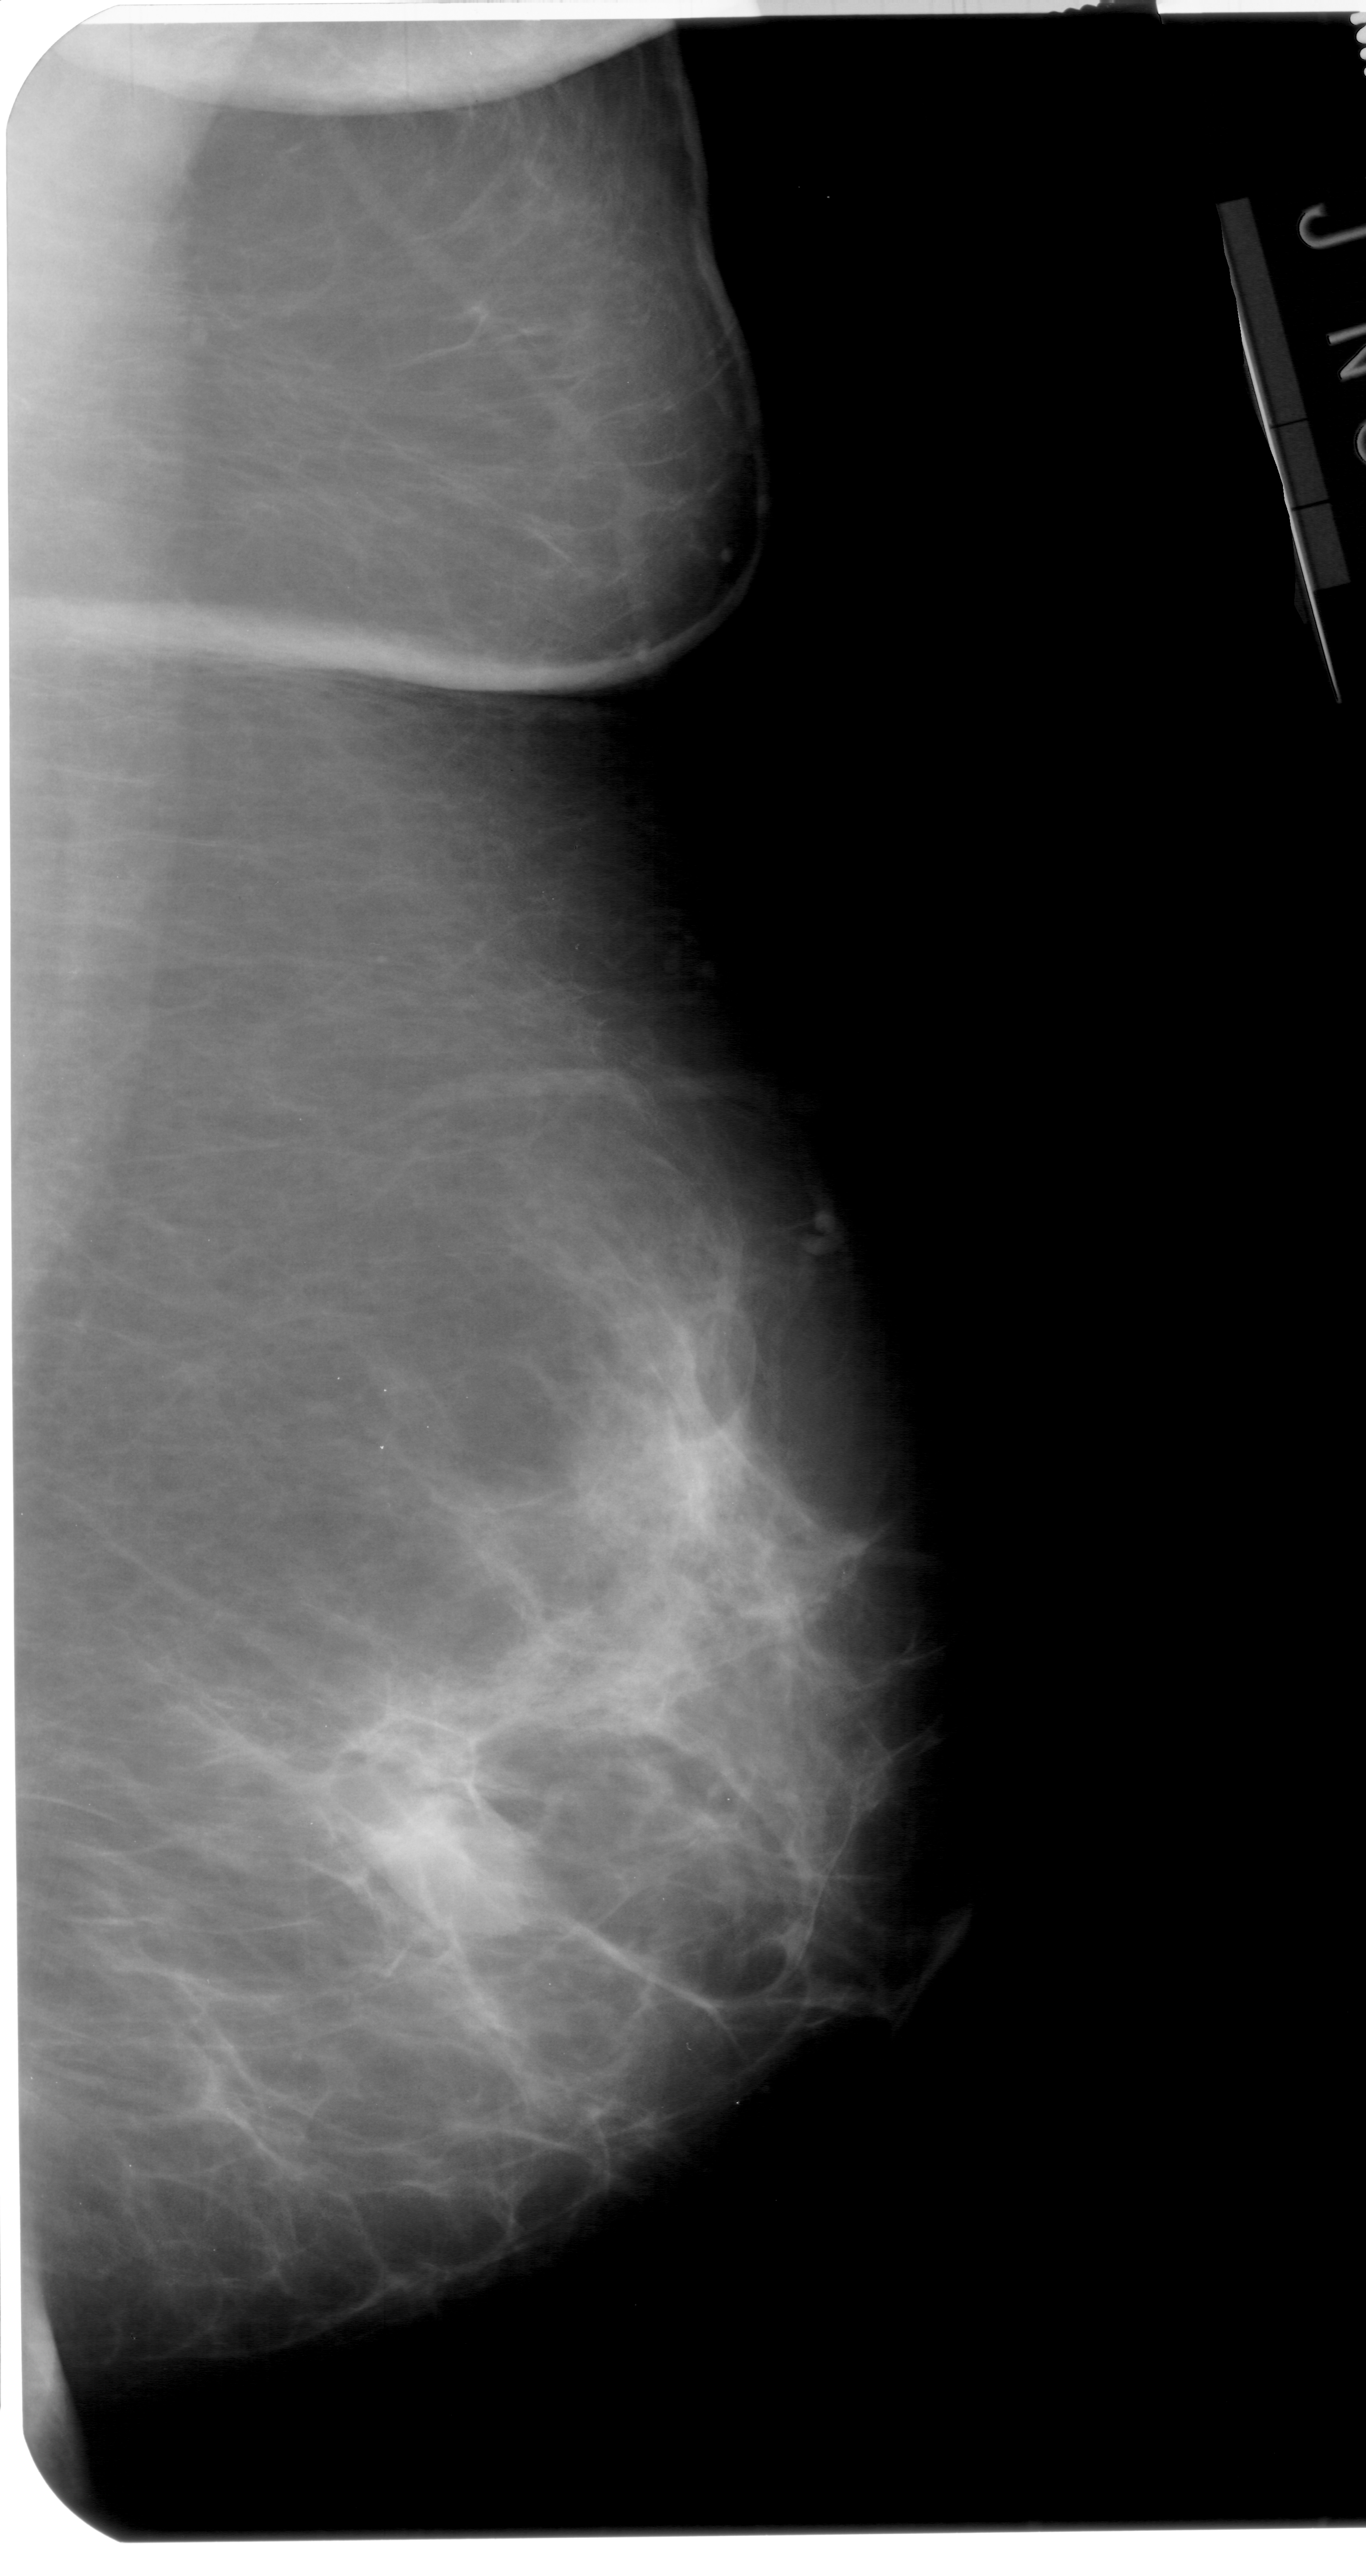
Mammogram (digitized film); right breast; MLO view; BI-RADS breast density category 3 (scale 1–4); 1366 × 2576 image matrix.
Expert-marked regions of interest on this film, with their recorded descriptors:
- mass, shape oval, margins circumscribed; BI-RADS assessment category 4; subtlety rating 5 on a 1 (subtle) to 5 (obvious) scale; pathology (as recorded): benign: bounding box [x1, y1, x2, y2] px = [325, 1784, 526, 1953]